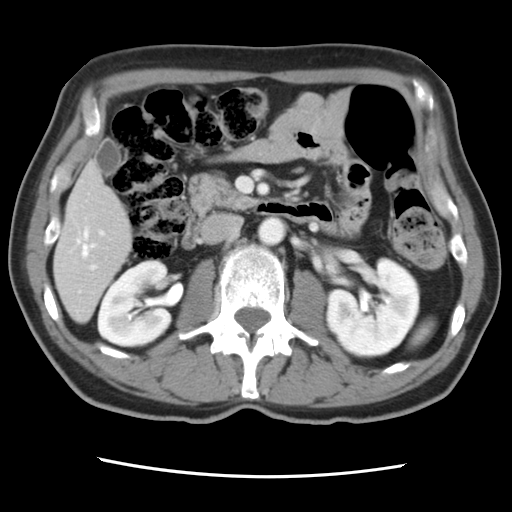
Contrast-enhanced abdominal CT, one axial slice. Intravenous contrast given. Soft-tissue window (W 400 / L 40 HU). 5 mm slice thickness. 512 × 512 image matrix, field of view 321 × 321 mm. Male patient, age 69 years. Case-level facts recorded for this patient, not image findings: diagnosis: colorectal cancer liver metastases, imaged before liver resection; multiple liver metastases: yes; largest metastasis: 3.5 cm.
Outlined on this slice (expert manual segmentation):
- hepatic veins: box from (x=77, y=229) to (x=95, y=257) px
- liver: (x=54, y=165)–(x=132, y=320)
- planned liver remnant (the part of the liver to remain after resection): (x=54, y=165)–(x=133, y=321)
- portal vein (with intrahepatic branches): (x=78, y=230)–(x=105, y=293)